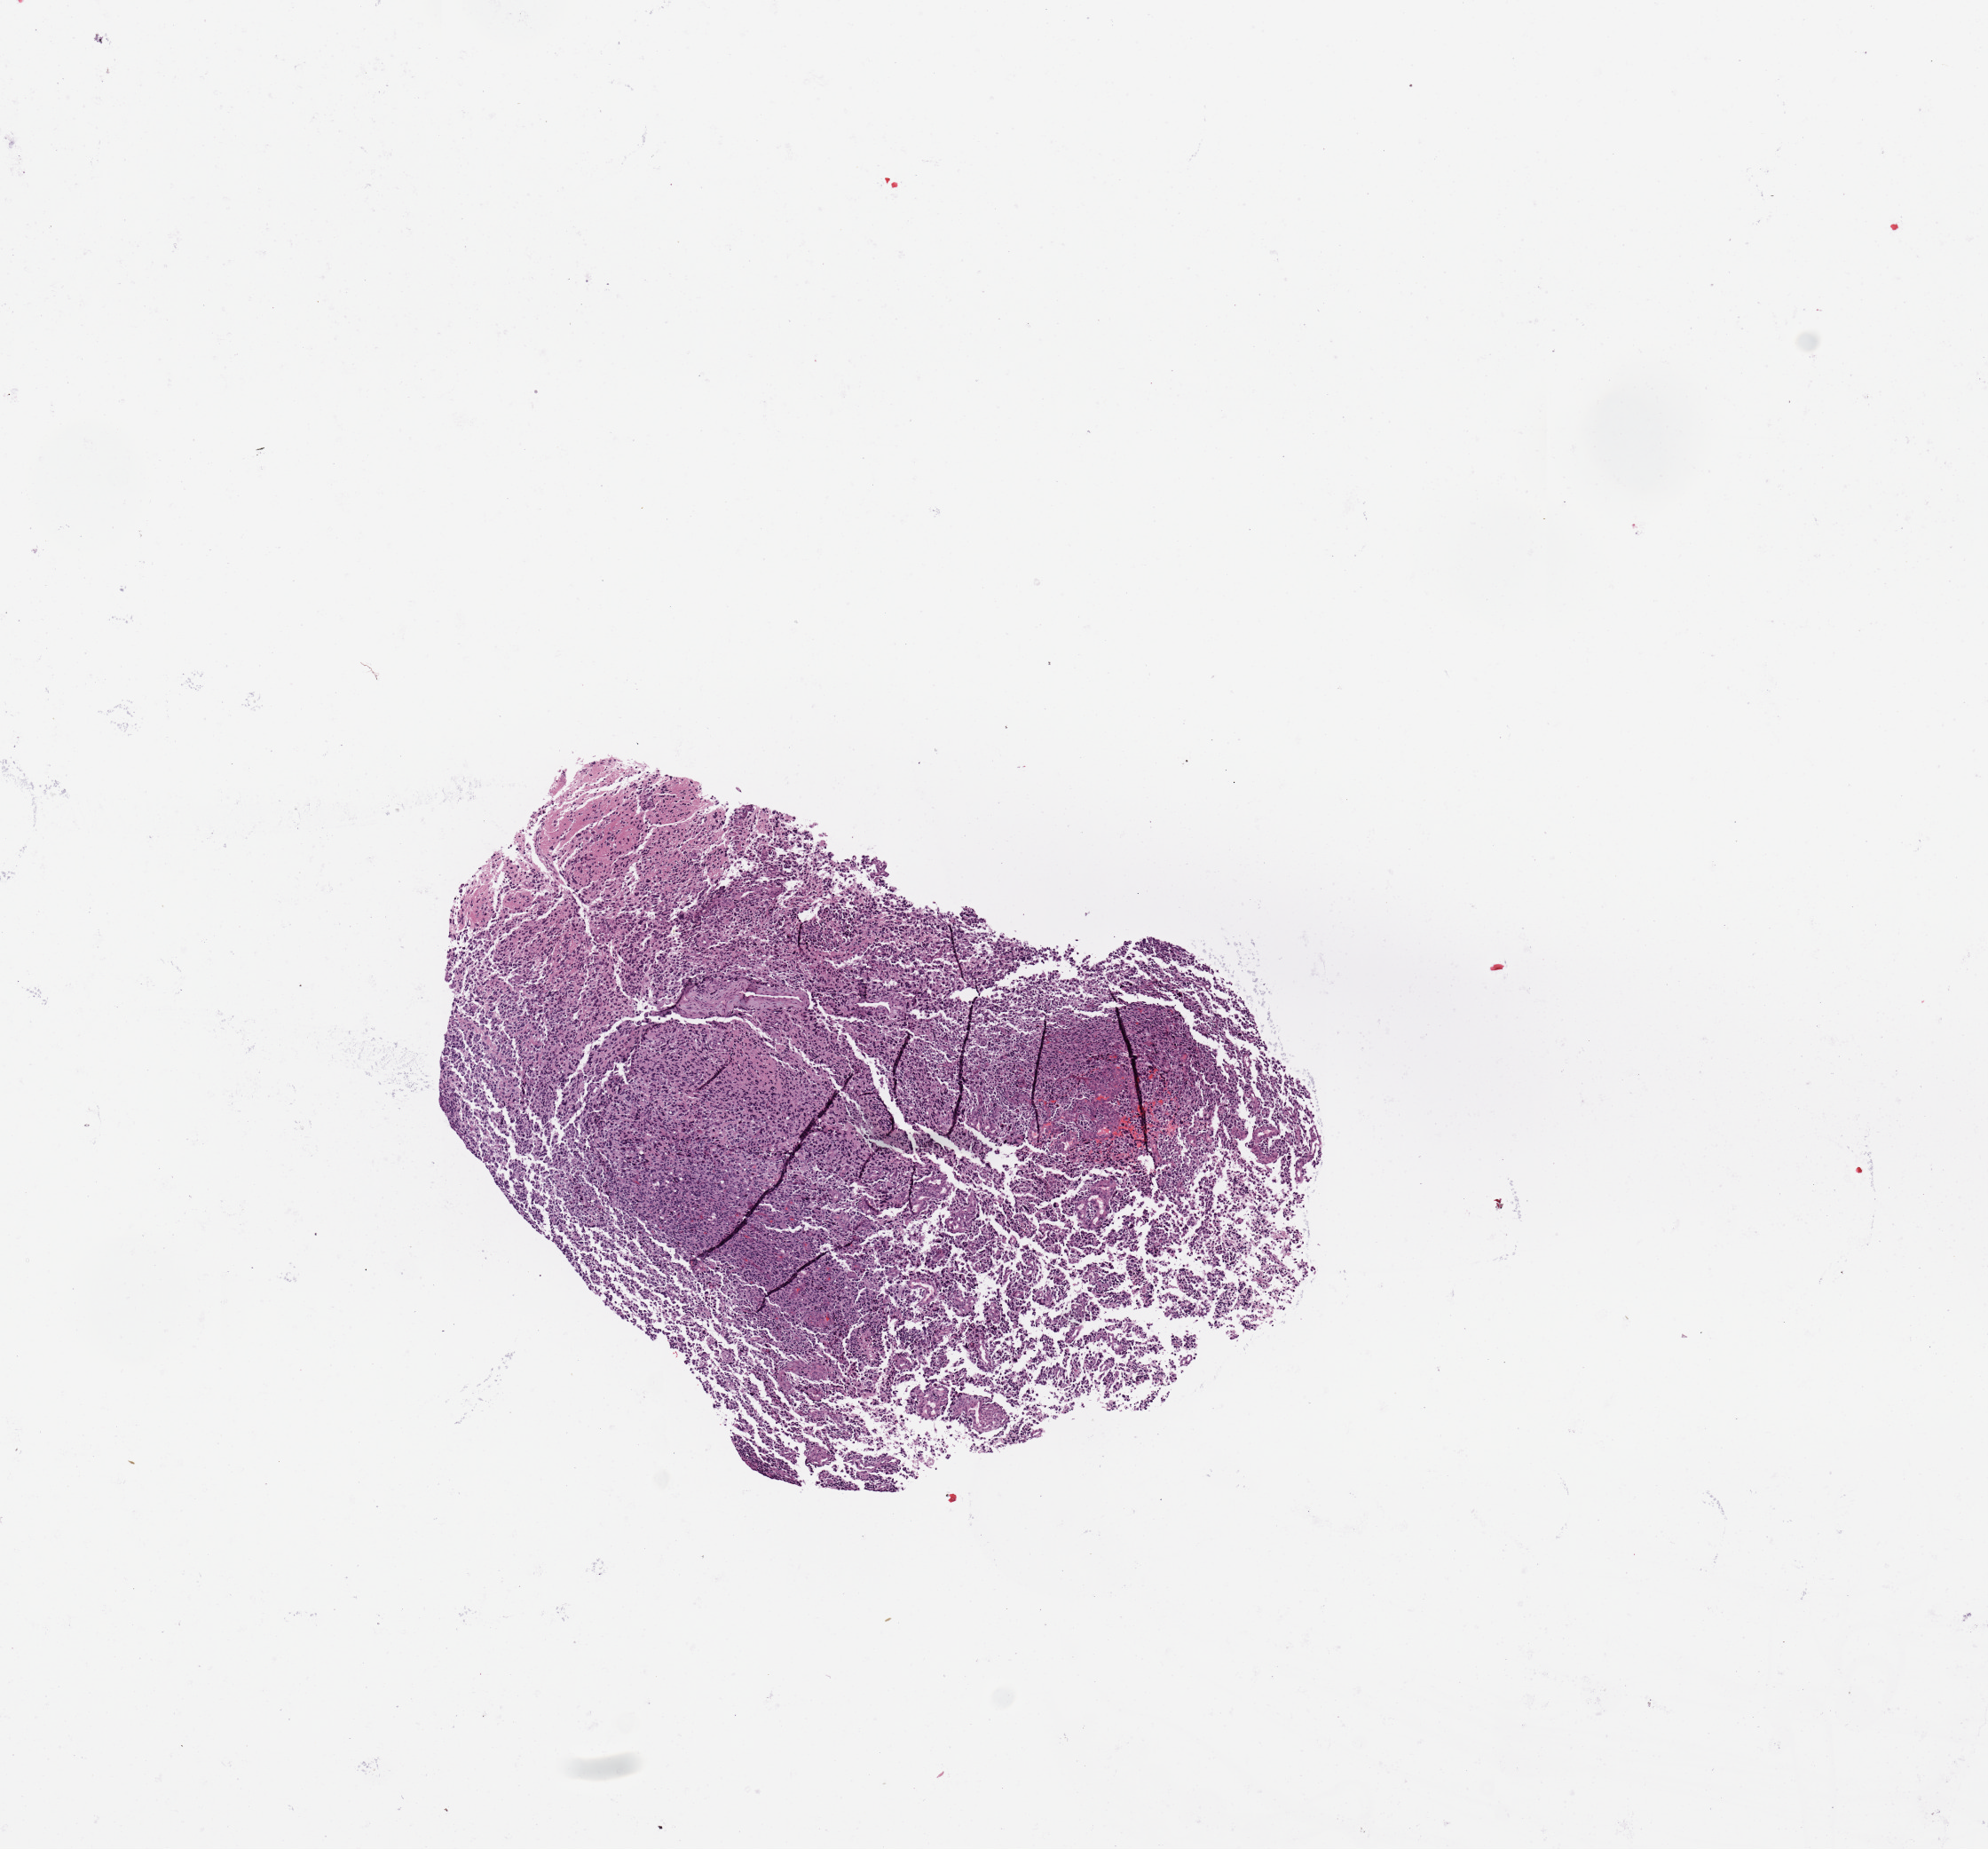
H&E-stained whole-slide image — whole scanned area (about 8.9 x 8.2 mm) shown as a low-resolution overview, brain, tumour tissue. Female, 30 y/o.
* histologic diagnosis: Glioblastoma